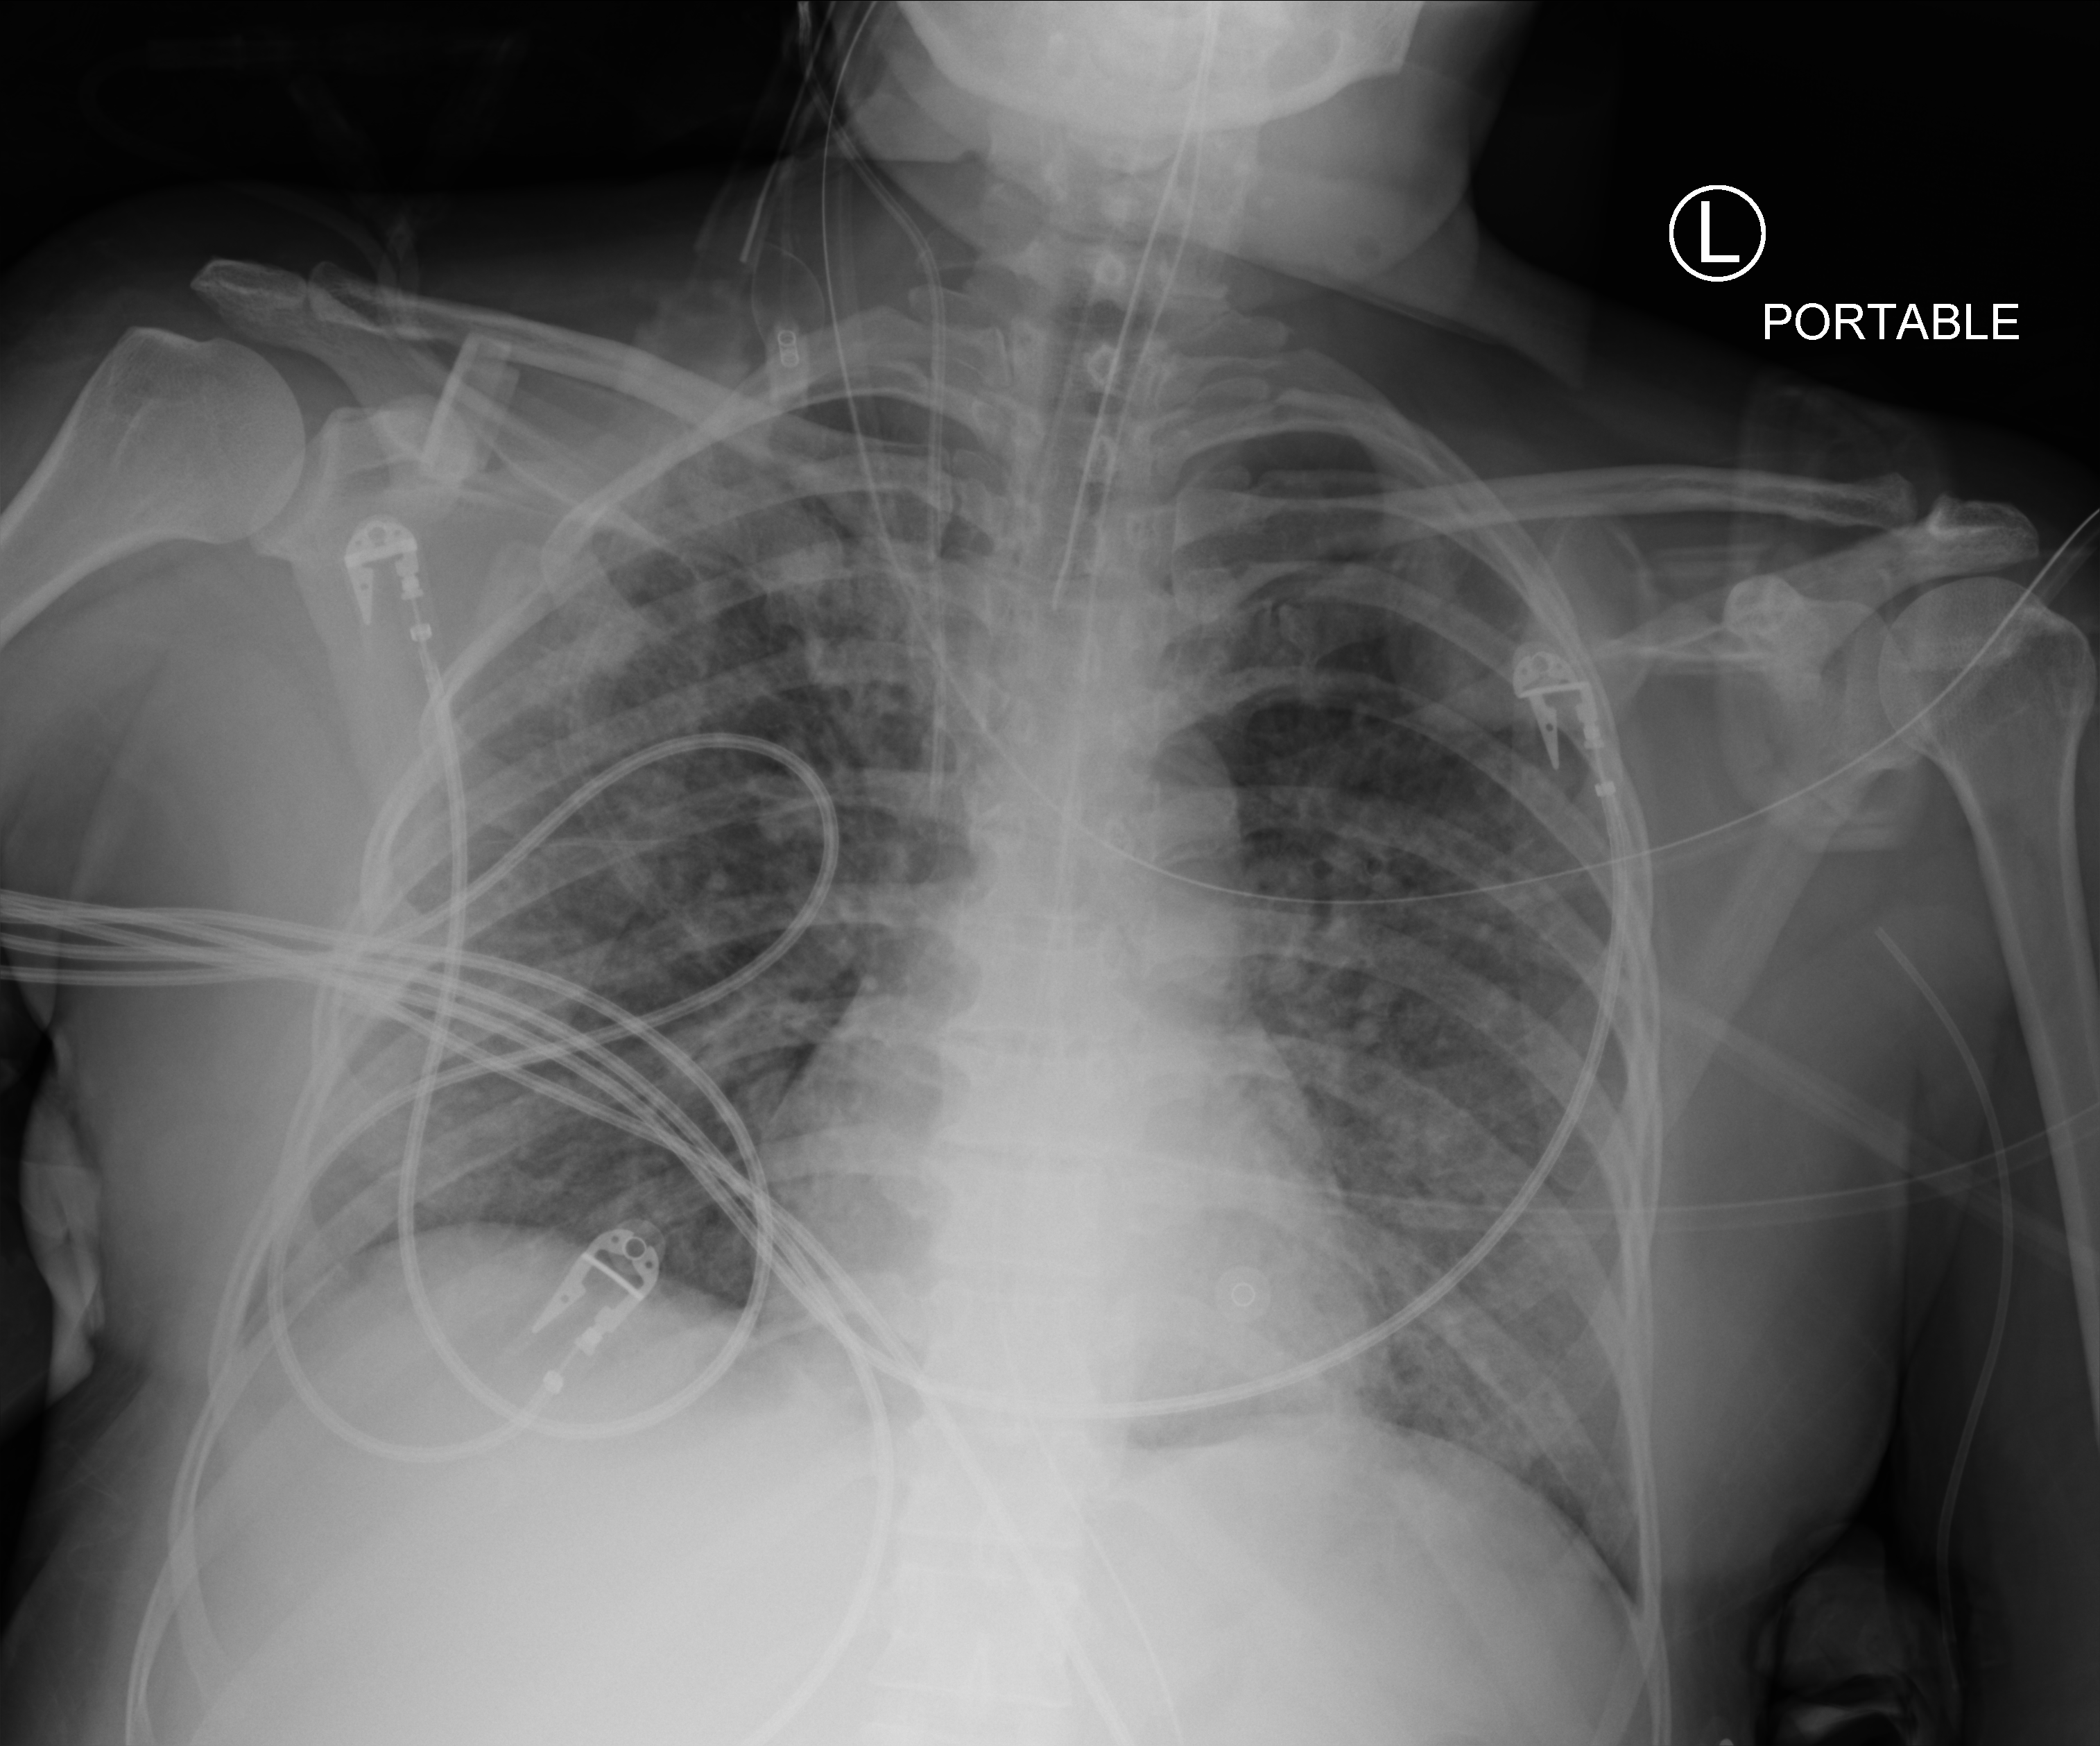
Bedside chest radiograph (computed radiography); anteroposterior (AP) projection. Patient hospitalised with COVID-19; female, aged 18–59 years.
From the hospital-stay record, not from the radiograph (when in the stay this image was taken is not recorded): admitted to intensive care during this hospital stay: yes; mechanically ventilated during this hospital stay: yes.